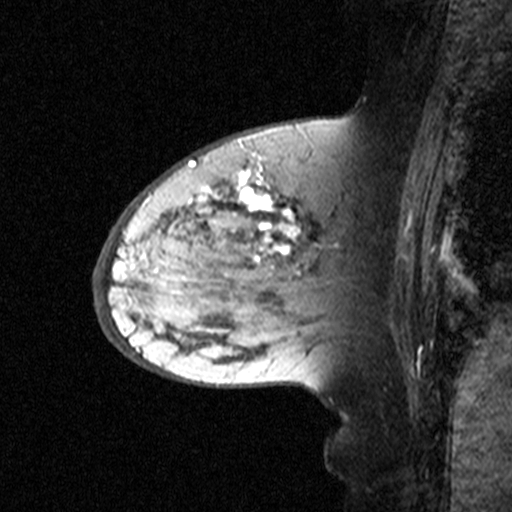
Breast MRI (dynamic contrast-enhanced), one sagittal slice. Position 20 of 44 along the scan axis. Dynamic contrast-enhanced study with each time point stored as its own series, time point 2 of 3 at this slice position (early post-contrast, ordered by acquisition time). 1.5 T. TE 4.5 ms, TR 11 ms. 512 × 512 image matrix, field of view 200 × 200 mm. Patient: female, 65 years. From the clinical record (not read from this slice): setting: breast cancer imaged before/during neoadjuvant chemotherapy; receptor status: HER2-positive.
Structures marked on this image (semi-automatically segmented with operator editing):
- analysis volume of interest (the breast-tissue region the enhancement analysis was run in; not a lesion): bounding box (x1, y1, x2, y2) in pixels: (160, 172, 329, 345)
- tumour enhancement mask (voxels above the 90 % enhancement threshold inside the analysis volume of interest): (179, 172, 298, 266)